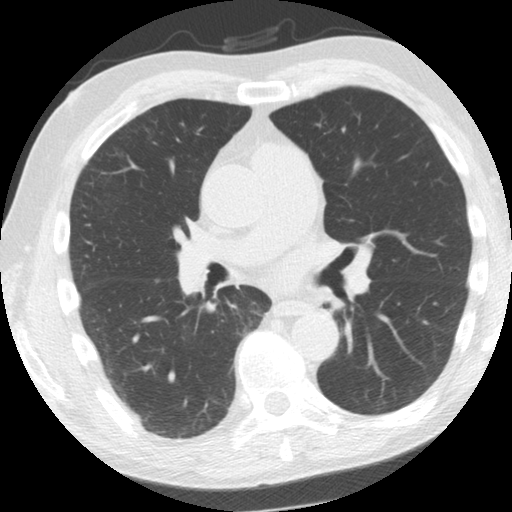
Chest CT (low-dose screening protocol), one axial image, second annual screen, lung window (W 1500 / L -600 HU), 2.5 mm slice thickness, slice 74 of 156 in the series, 512 × 512 image matrix. Male participant, aged 61 years at enrolment. Former smoker at enrolment.
• Expert-annotated lung lesion, bounding box <300,290,347,328> (left, top, right, bottom; pixels).
• Screening reader's record for this exam: no non-calcified nodule ≥4 mm recorded.
• Participant outcome: lung cancer diagnosed 775 days after this screen (after the third annual screen) — squamous cell carcinoma, NOS, left upper lobe, left lower lobe, well differentiated (G1), stage IIB (AJCC 6th edition), 100 mm at pathology.